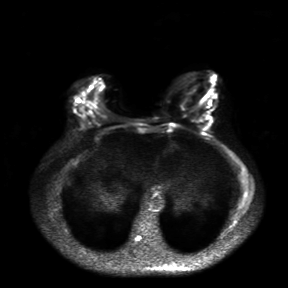
Breast MRI, one axial slice. Position 8 of 30 along the scan axis. Diffusion-weighted series; image 2 of 4 stored at this slice position (different b-values; order by instance number). 3 T. 4 mm slice thickness. 288 × 288 image matrix, field of view 360 × 360 mm. Female patient.
Annotated regions visible in this slice (expert manual segmentation):
- tumour on diffusion-weighted imaging: bounding box (x1, y1, x2, y2) in pixels: (194, 107, 208, 128)